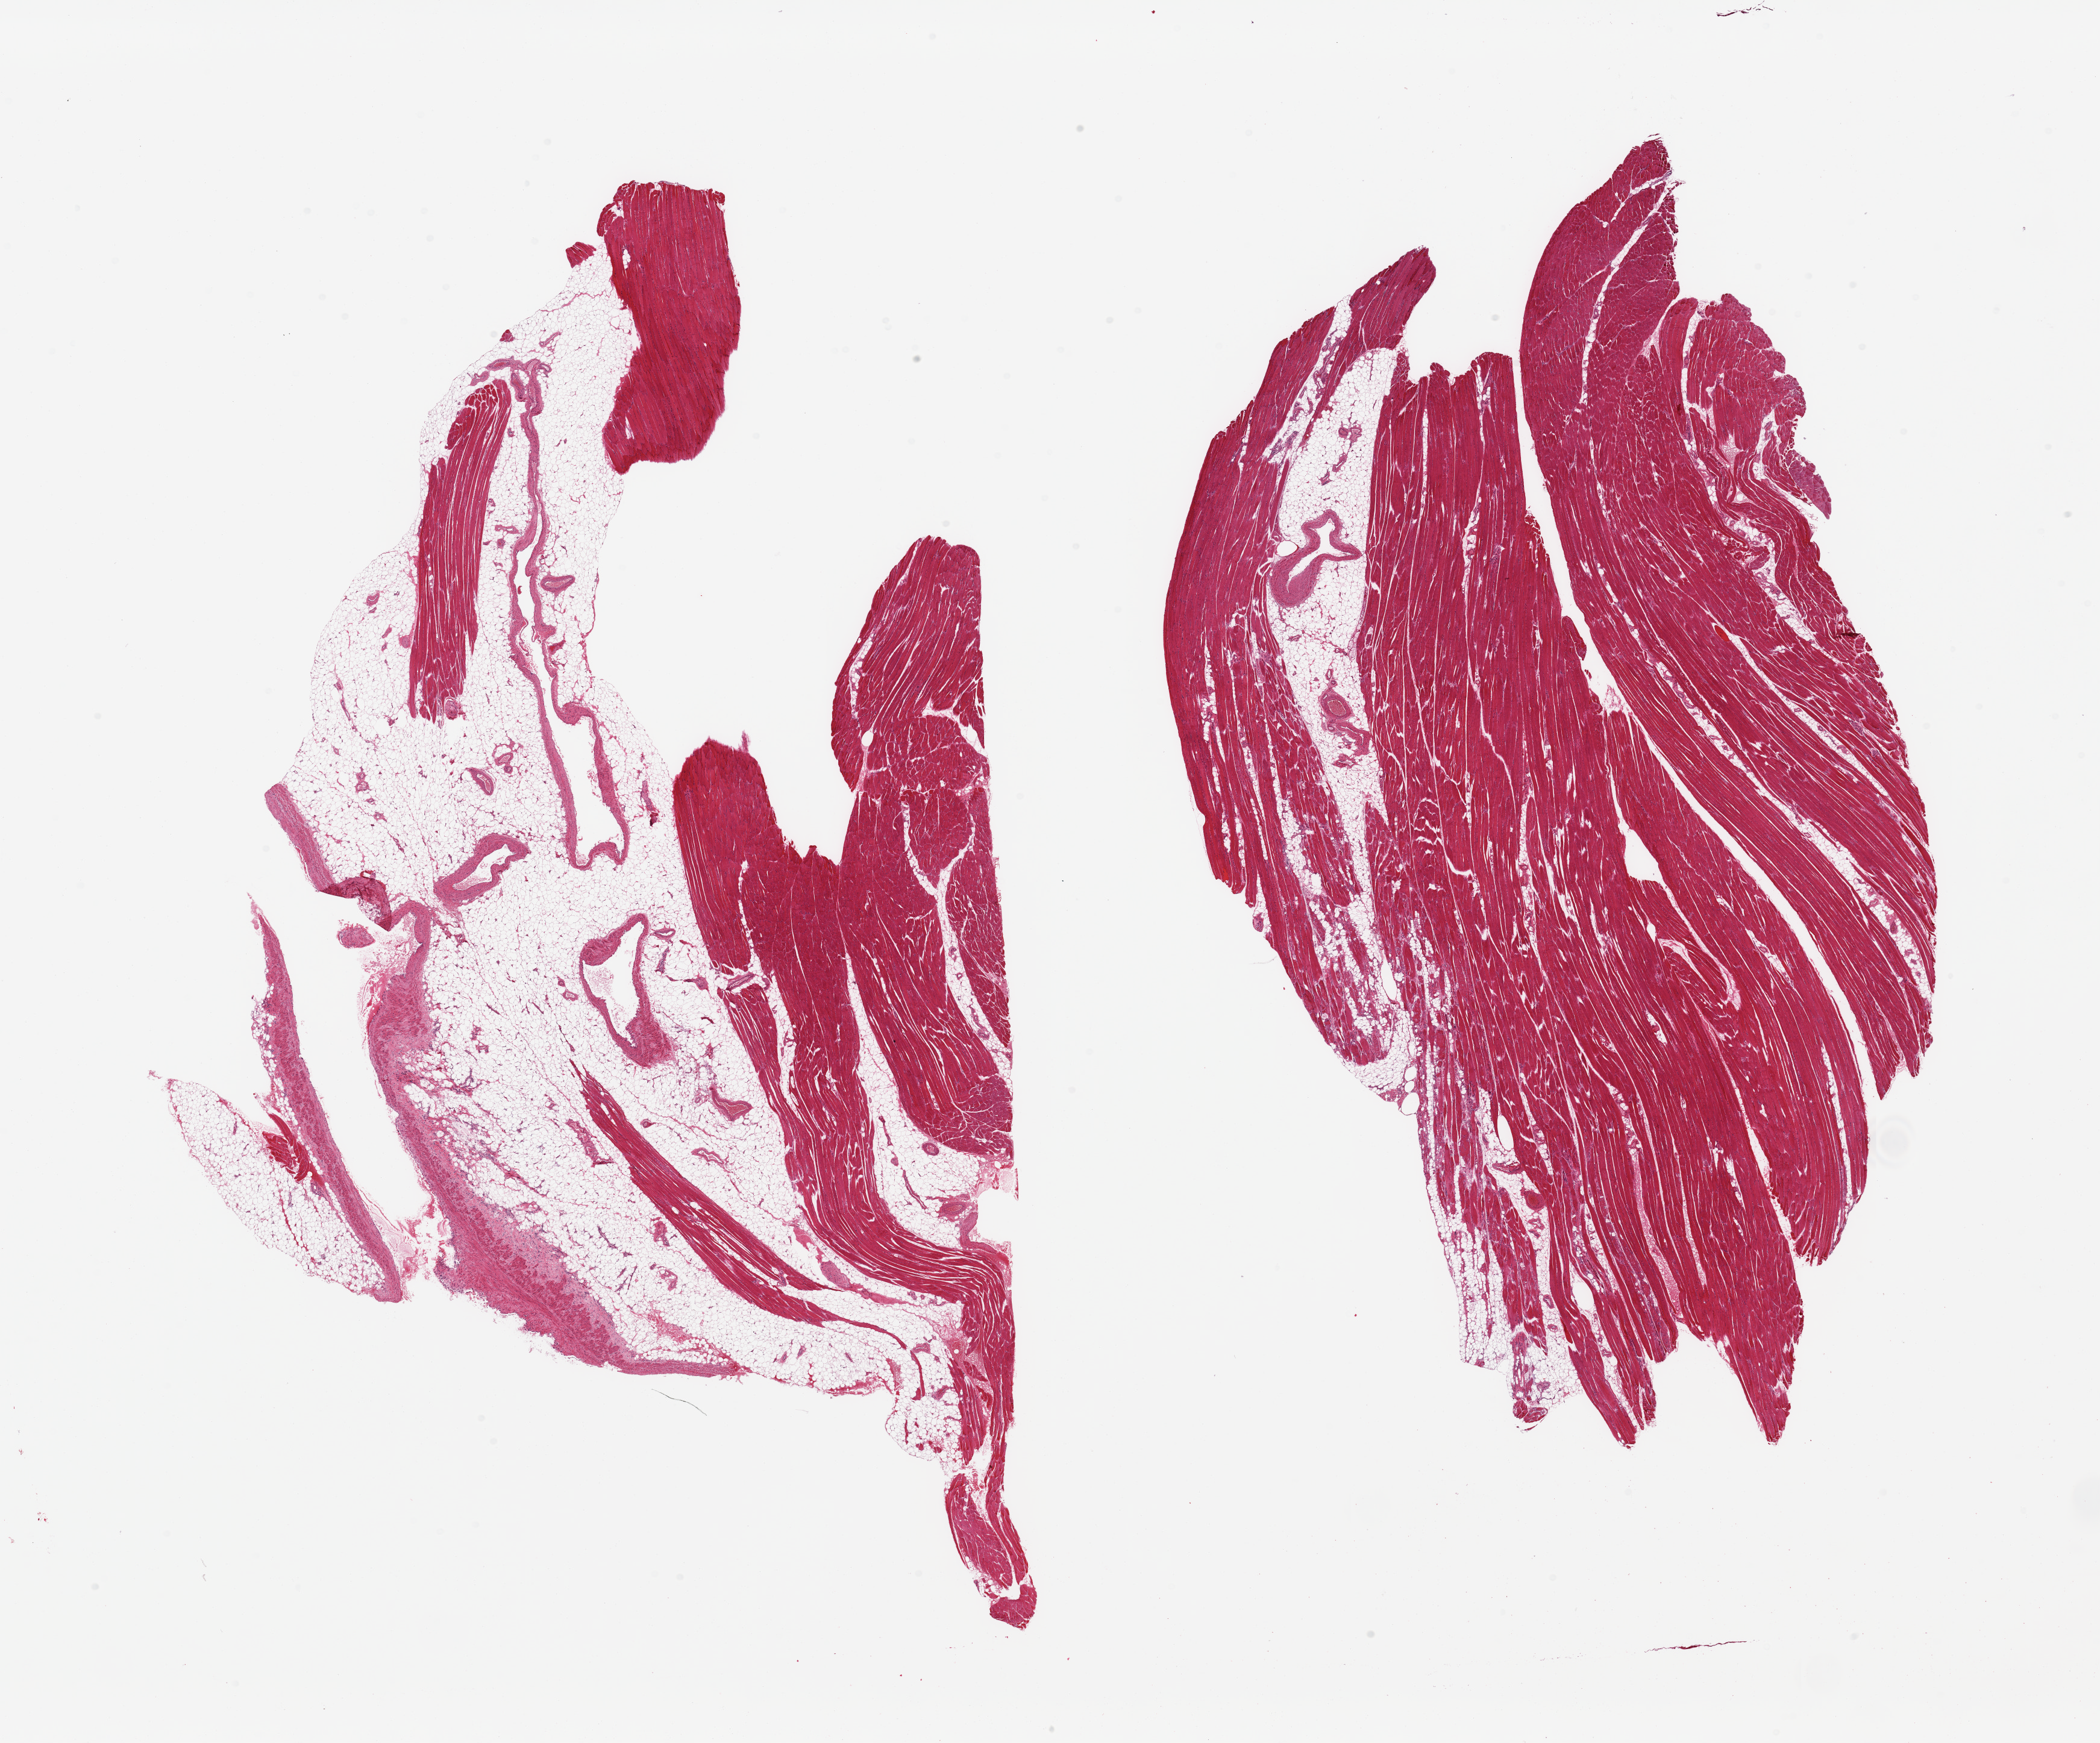
Whole-slide image, H&E stain — shown as a low-resolution overview of the whole scanned area (about 27.6 x 22.9 mm, acquisition: 20x scan). PAXgene-fixed, paraffin-embedded tissue. Section of skeletal muscle (target tissue). Tissue donor sample.
• reviewer comment on this tissue sample: 2 pieces; 60% and 10% internal fat